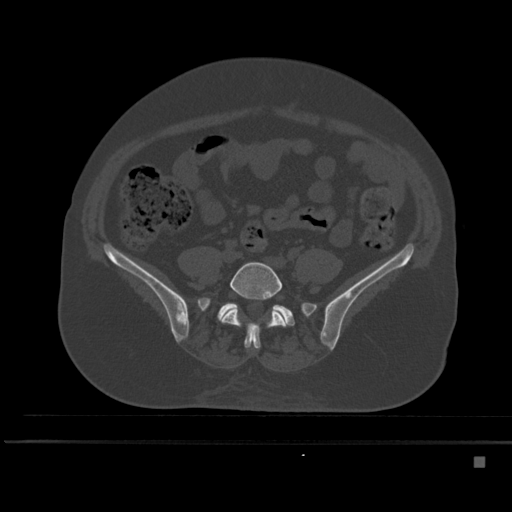
CT including the spine, one axial slice; position 105 of 495 along the scan axis; bone window (W 1800 / L 400 HU); 1.5 mm slice thickness; 512 × 512 image matrix, field of view 404 × 404 mm. Patient: female, 33 years. From the clinical record (not read from this slice): primary cancer: breast; vertebrae with lytic lesions (as recorded): T1.
Annotated regions visible in this slice (semi-automatically segmented with operator editing):
- L5 vertebra: bounding box (x1, y1, x2, y2) in pixels: (220, 261, 287, 349)